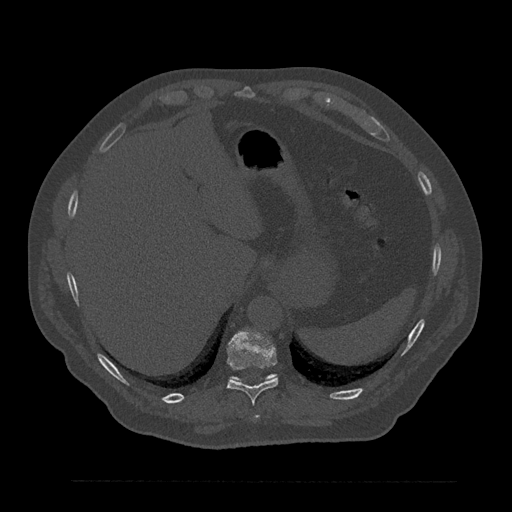
CT including the spine, one axial slice; position 337 of 797 along the scan axis; bone window (W 1800 / L 400 HU); 0.5 mm slice thickness; 512 × 512 image matrix. Male patient, age 61 years. Case-level facts recorded for this patient, not image findings: primary cancer: prostate.
Annotated regions visible in this slice (semi-automatically segmented with operator editing):
- T10 vertebra: bounding box (x1, y1, x2, y2) in pixels: (227, 329, 278, 405)
- T11 vertebra: (230, 374, 276, 381)
- T9 vertebra: (254, 416, 259, 419)